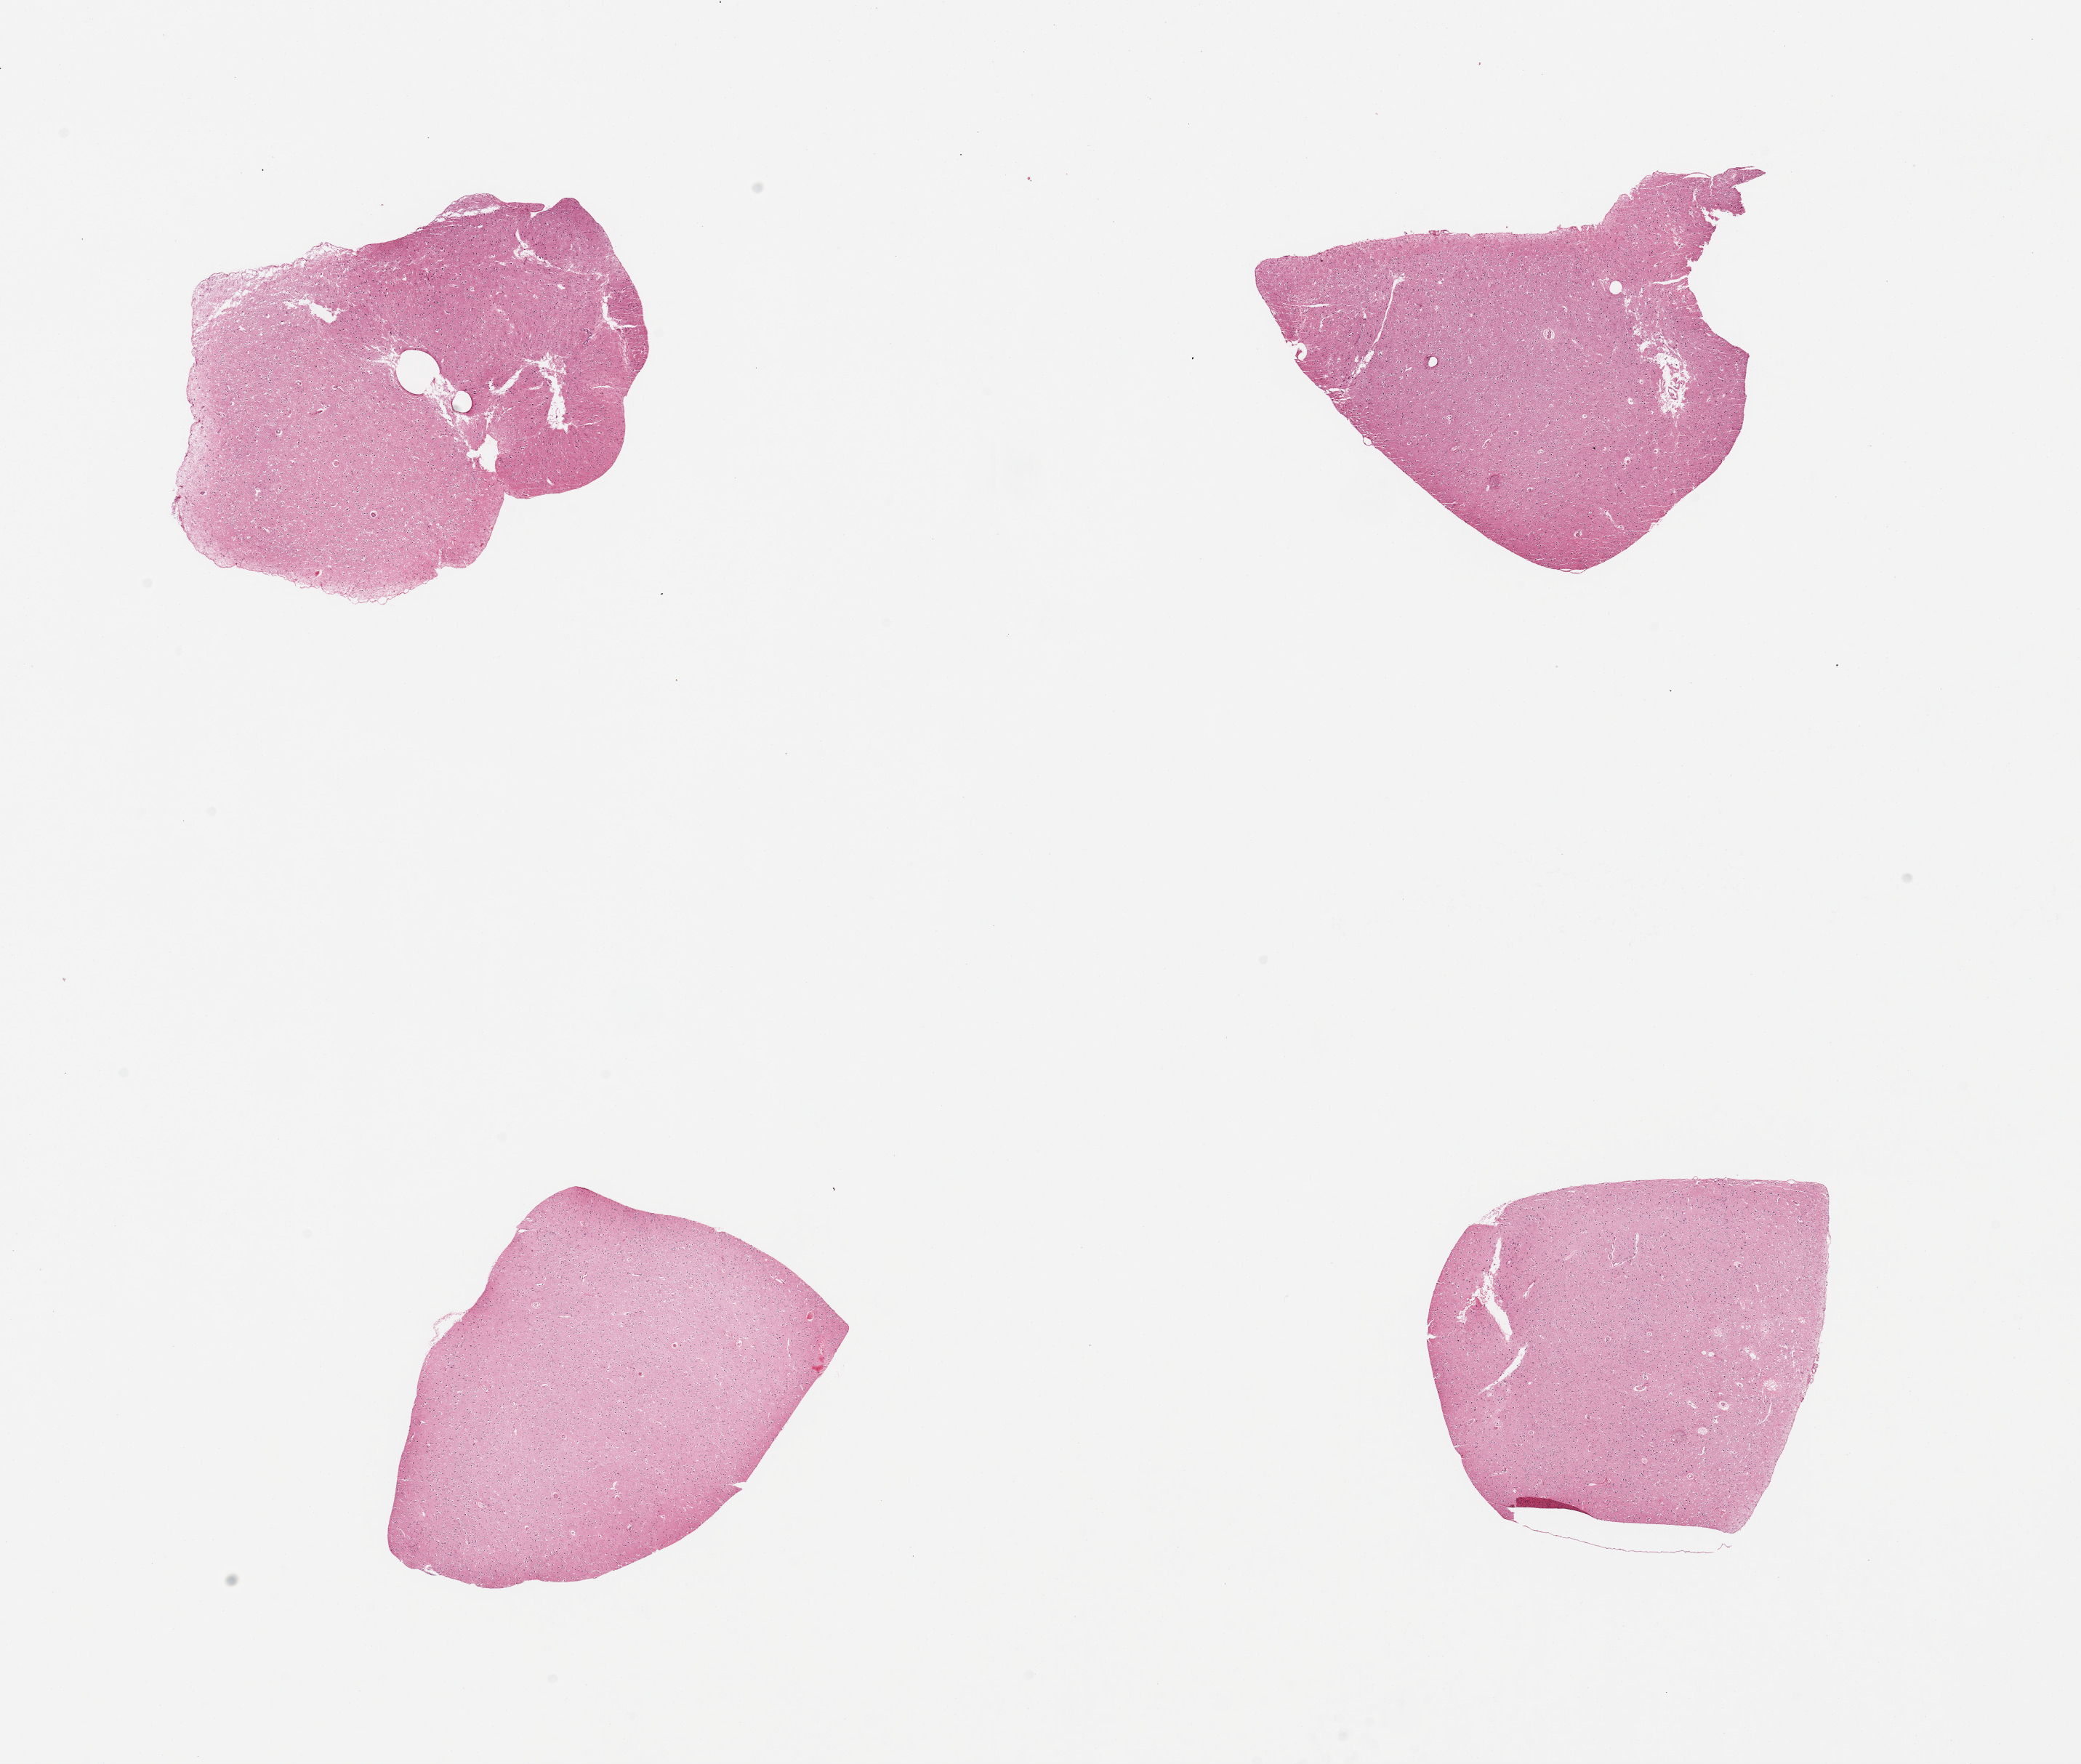
Digitized haematoxylin and eosin-stained section — low-resolution overview of the scanned area, about 22.6 x 19.2 mm. PAXgene-fixed paraffin-embedded (PFPE) section. Target tissue: cerebral cortex. Donor tissue sample.
Review note (as recorded): 4 pieces, no abnormalities.